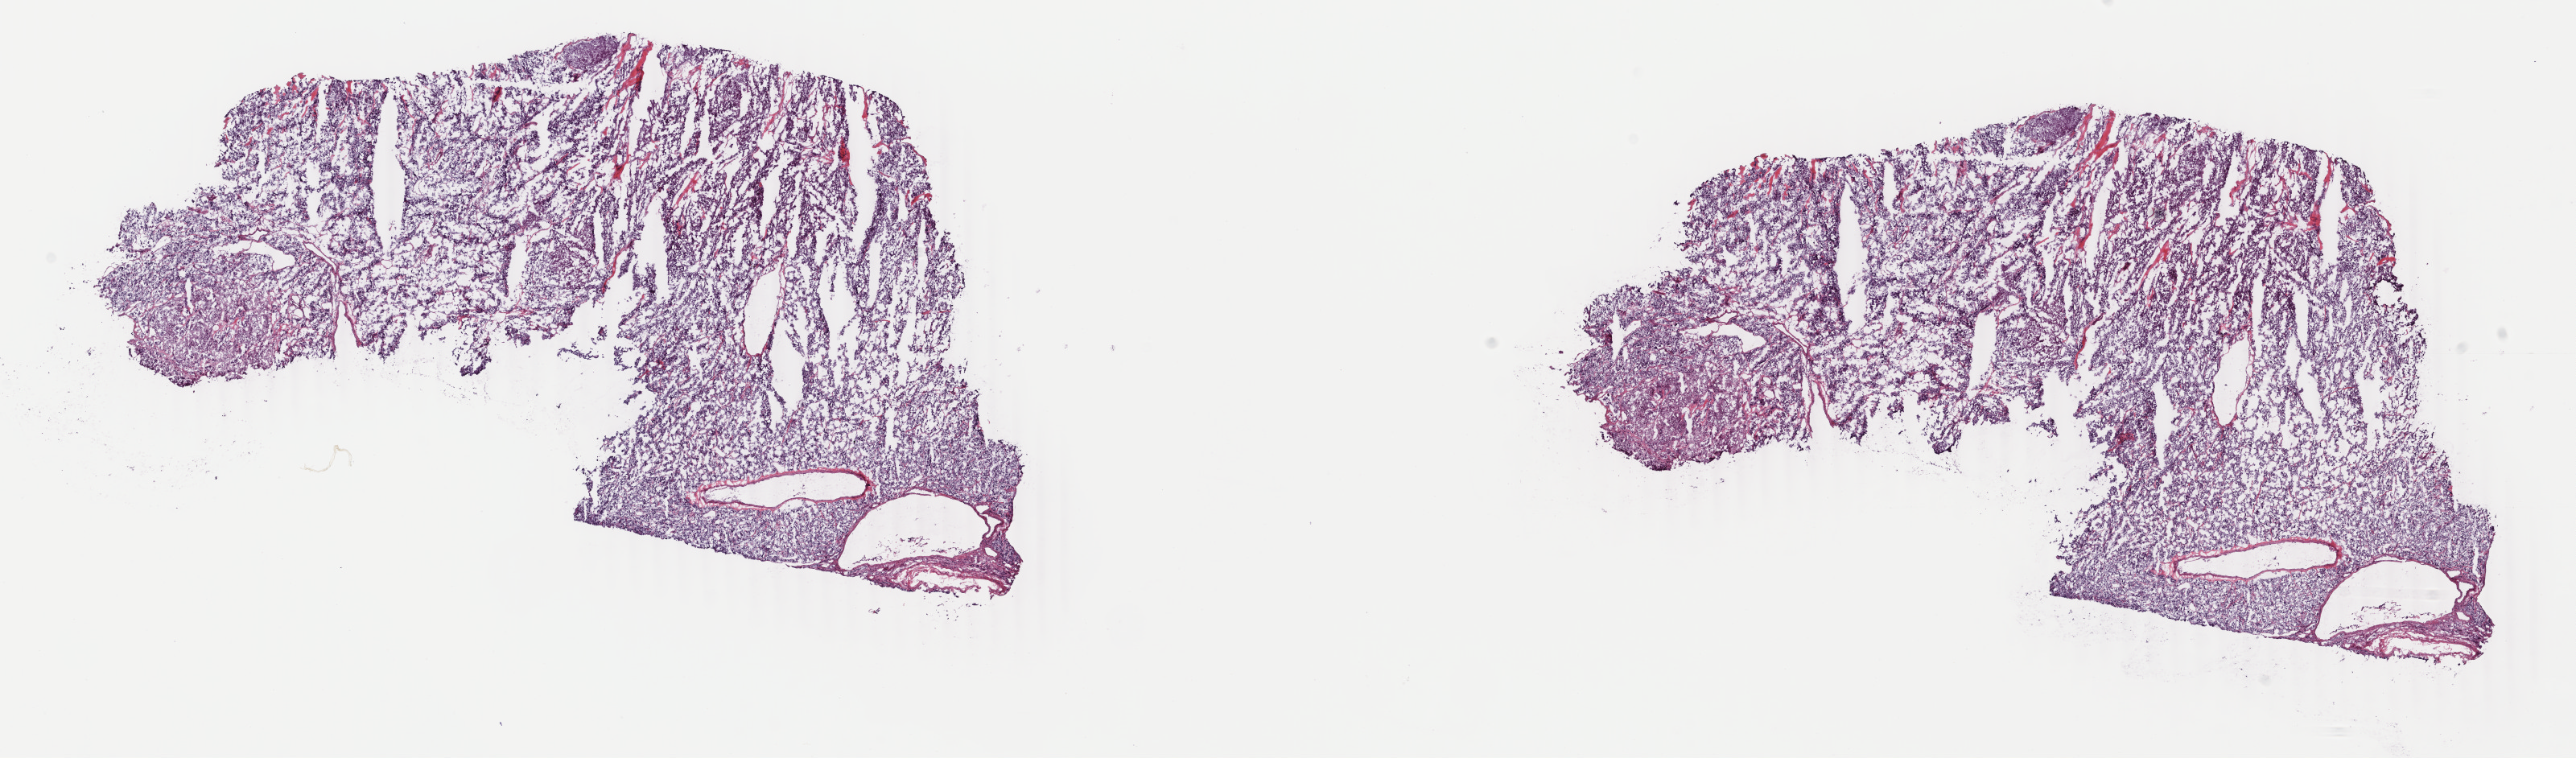
Digitized H&E tissue section (whole slide), low-resolution overview of the scanned area, about 25.5 x 7.5 mm (from a 40x scan). Frozen section from the top of the tissue portion. Primary tumour sample from the adrenal gland. Female patient; age at initial diagnosis 70 years. Pathologist review of this section (percent, as recorded): tumour cells 100%, tumour nuclei 80%, normal cells 0%, stromal cells 0%, necrosis 0%. Infiltration values recorded for this section: lymphocyte infiltration 1%, monocyte infiltration 0%, neutrophil infiltration 0%.
* laterality: right
* histologic diagnosis: Pheochromocytoma, NOS